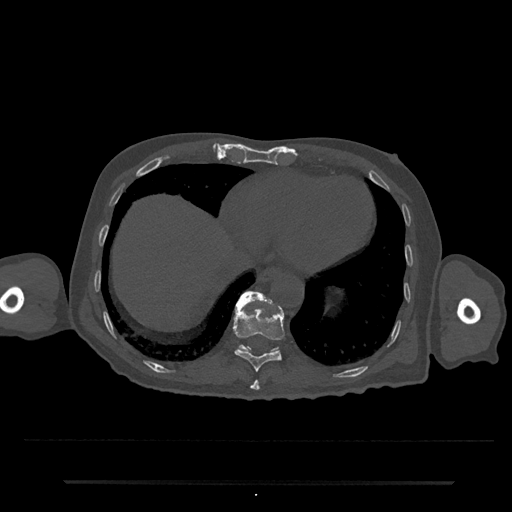
CT including the spine, one axial slice; slice 302 of 797 in the series (ordered by position); 120 kVp; bone window (W 1800 / L 400 HU); 0.5 mm slice thickness; 512 × 512 image matrix, field of view 427 × 427 mm. Male patient, age 74 years. From the clinical record (not read from this slice): primary cancer: prostate.
Annotated regions visible in this slice (semi-automatically segmented with operator editing):
- T10 vertebra: bounding box [x1, y1, x2, y2] px = [233, 306, 285, 372]
- T11 vertebra: [235, 291, 279, 353]
- T9 vertebra: [250, 380, 260, 391]